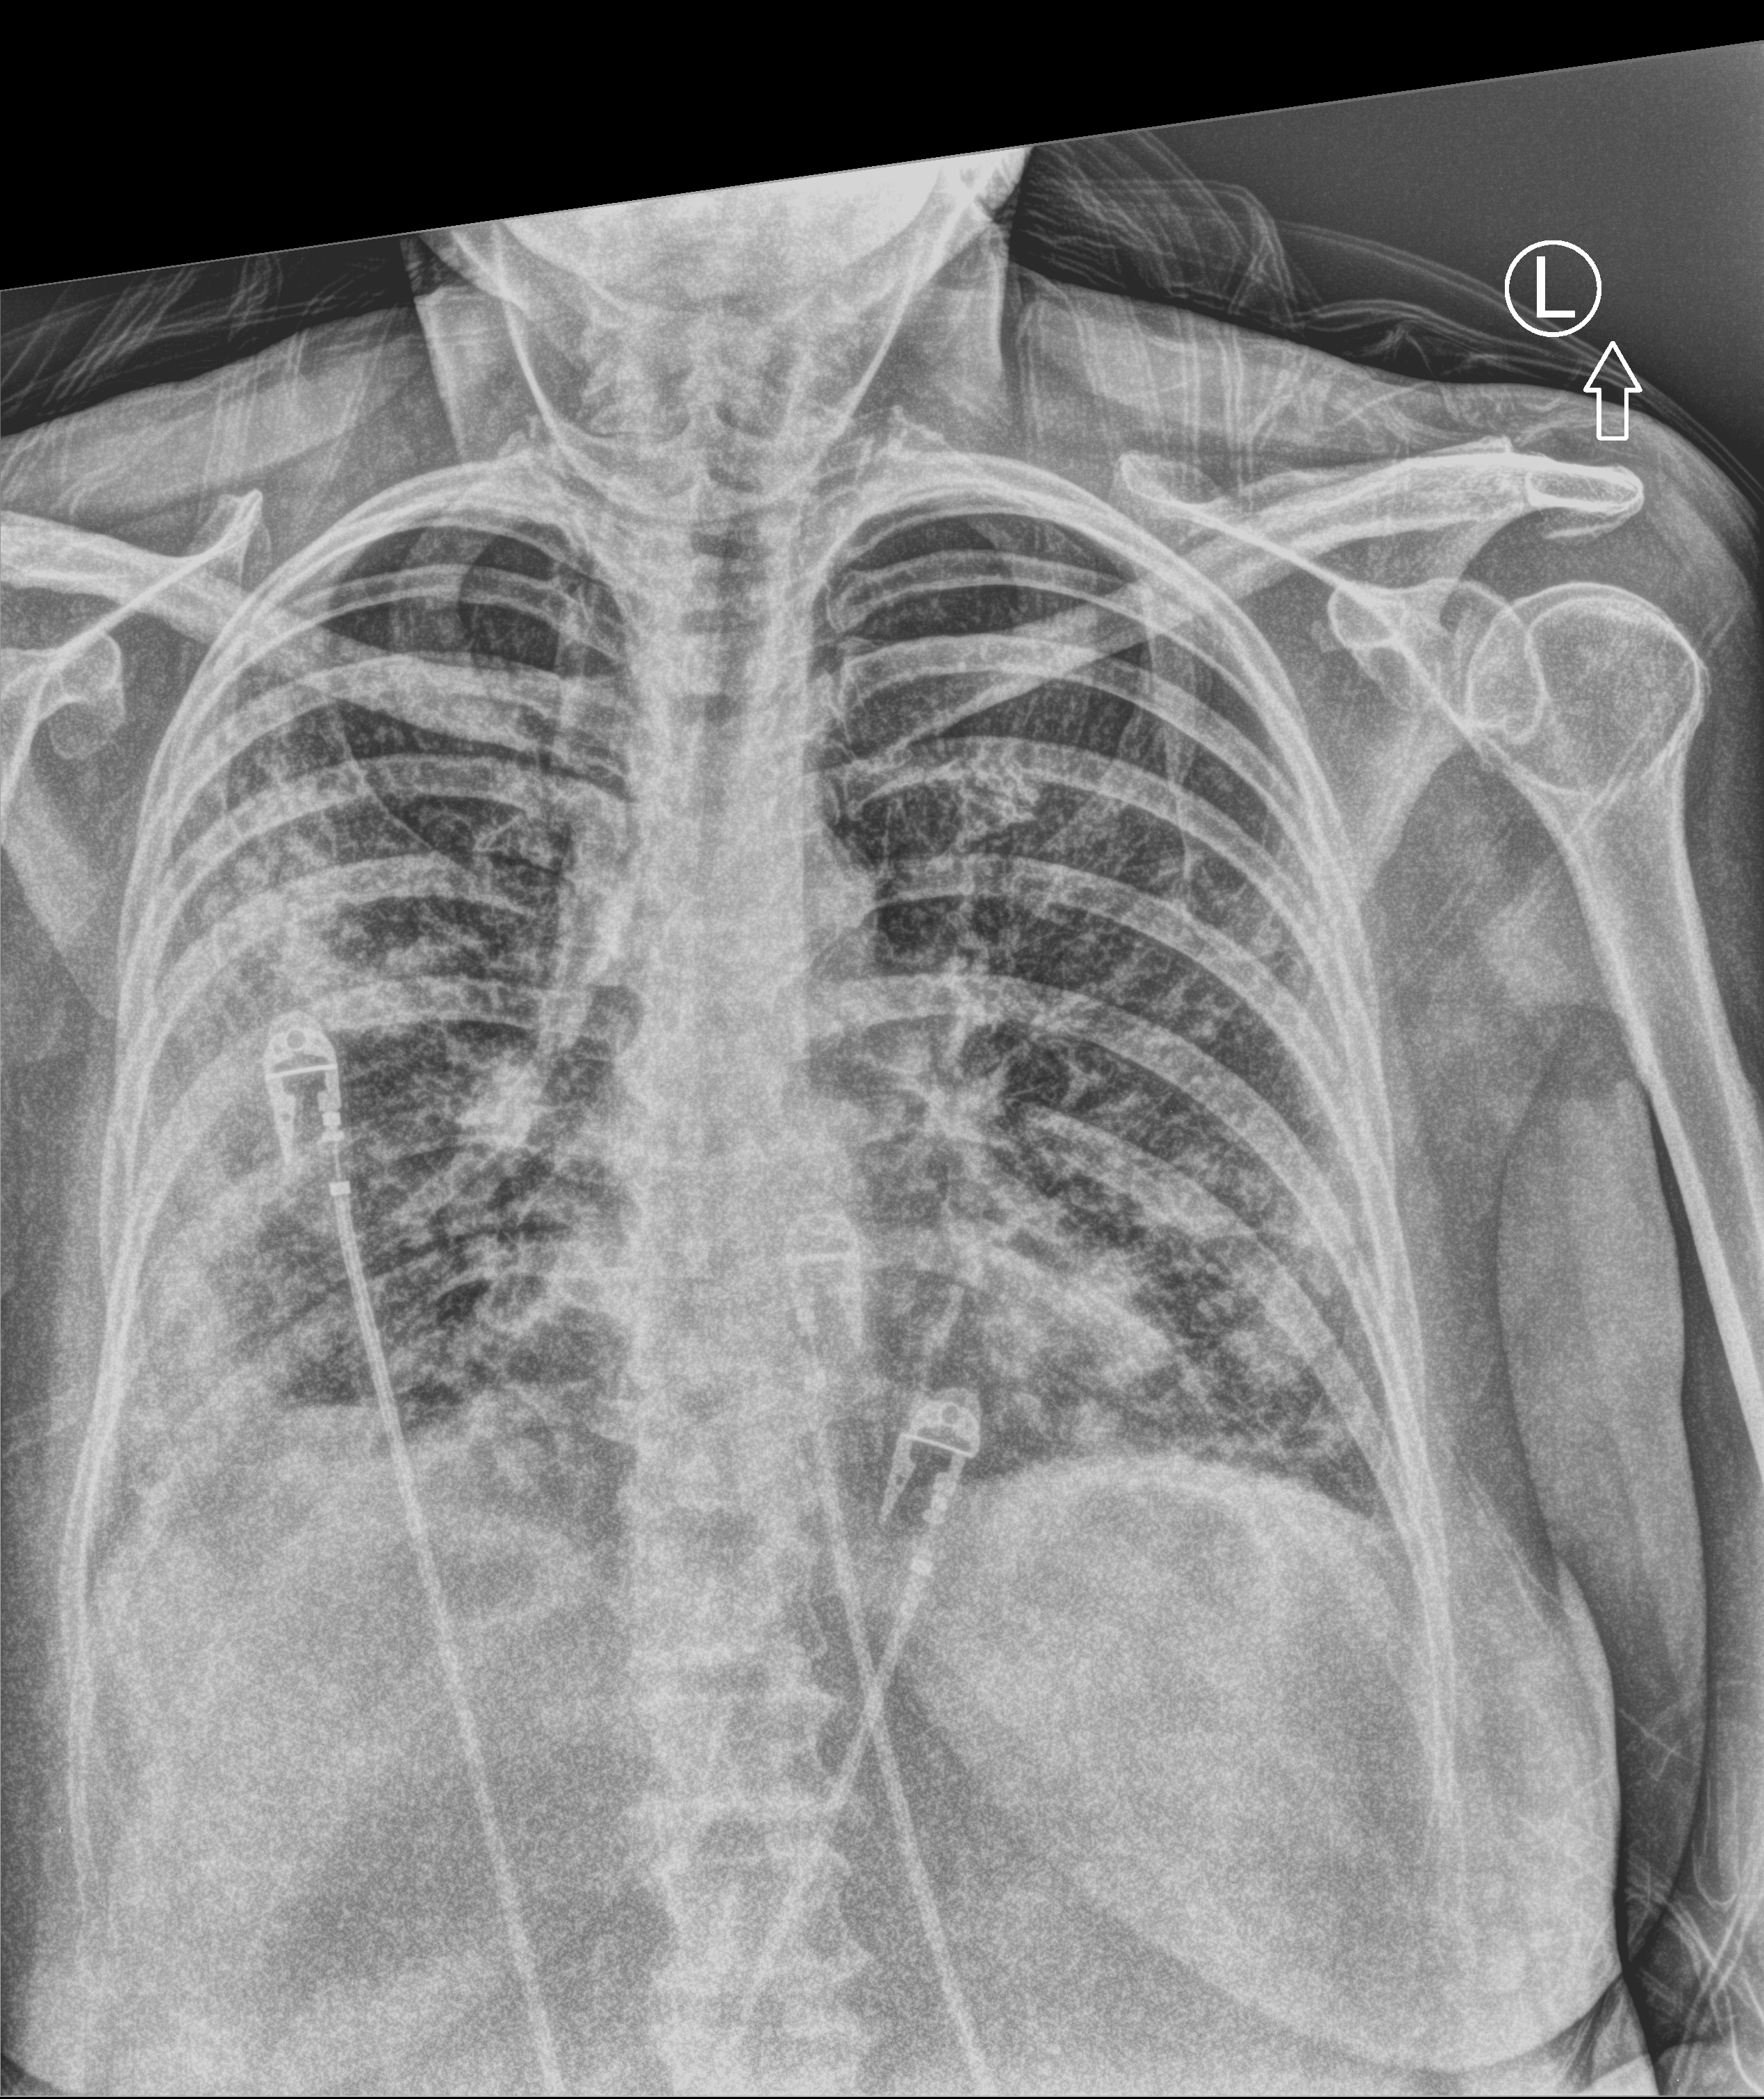
Portable chest radiograph. Female patient hospitalised with COVID-19, age 60–74 years.
Admission-level facts for this patient (not findings on this image; timing relative to this image not recorded): admitted to intensive care during this hospital stay: no; COPD (admission record): no.